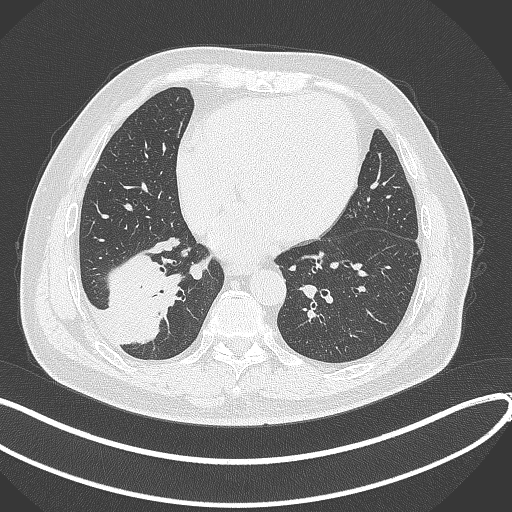
Chest CT, one axial slice; position 126 of 360 along the scan axis; reconstruction kernel B70f; 120 kVp; lung window (W 1500 / L -600 HU); 1 mm slice thickness; 512 × 512 image matrix. Male patient, age 59 years.
Structures marked on this image (bounding box drawn by a radiologist):
- lung tumour (recorded histology: adenocarcinoma): box from (x=108, y=252) to (x=181, y=347) px